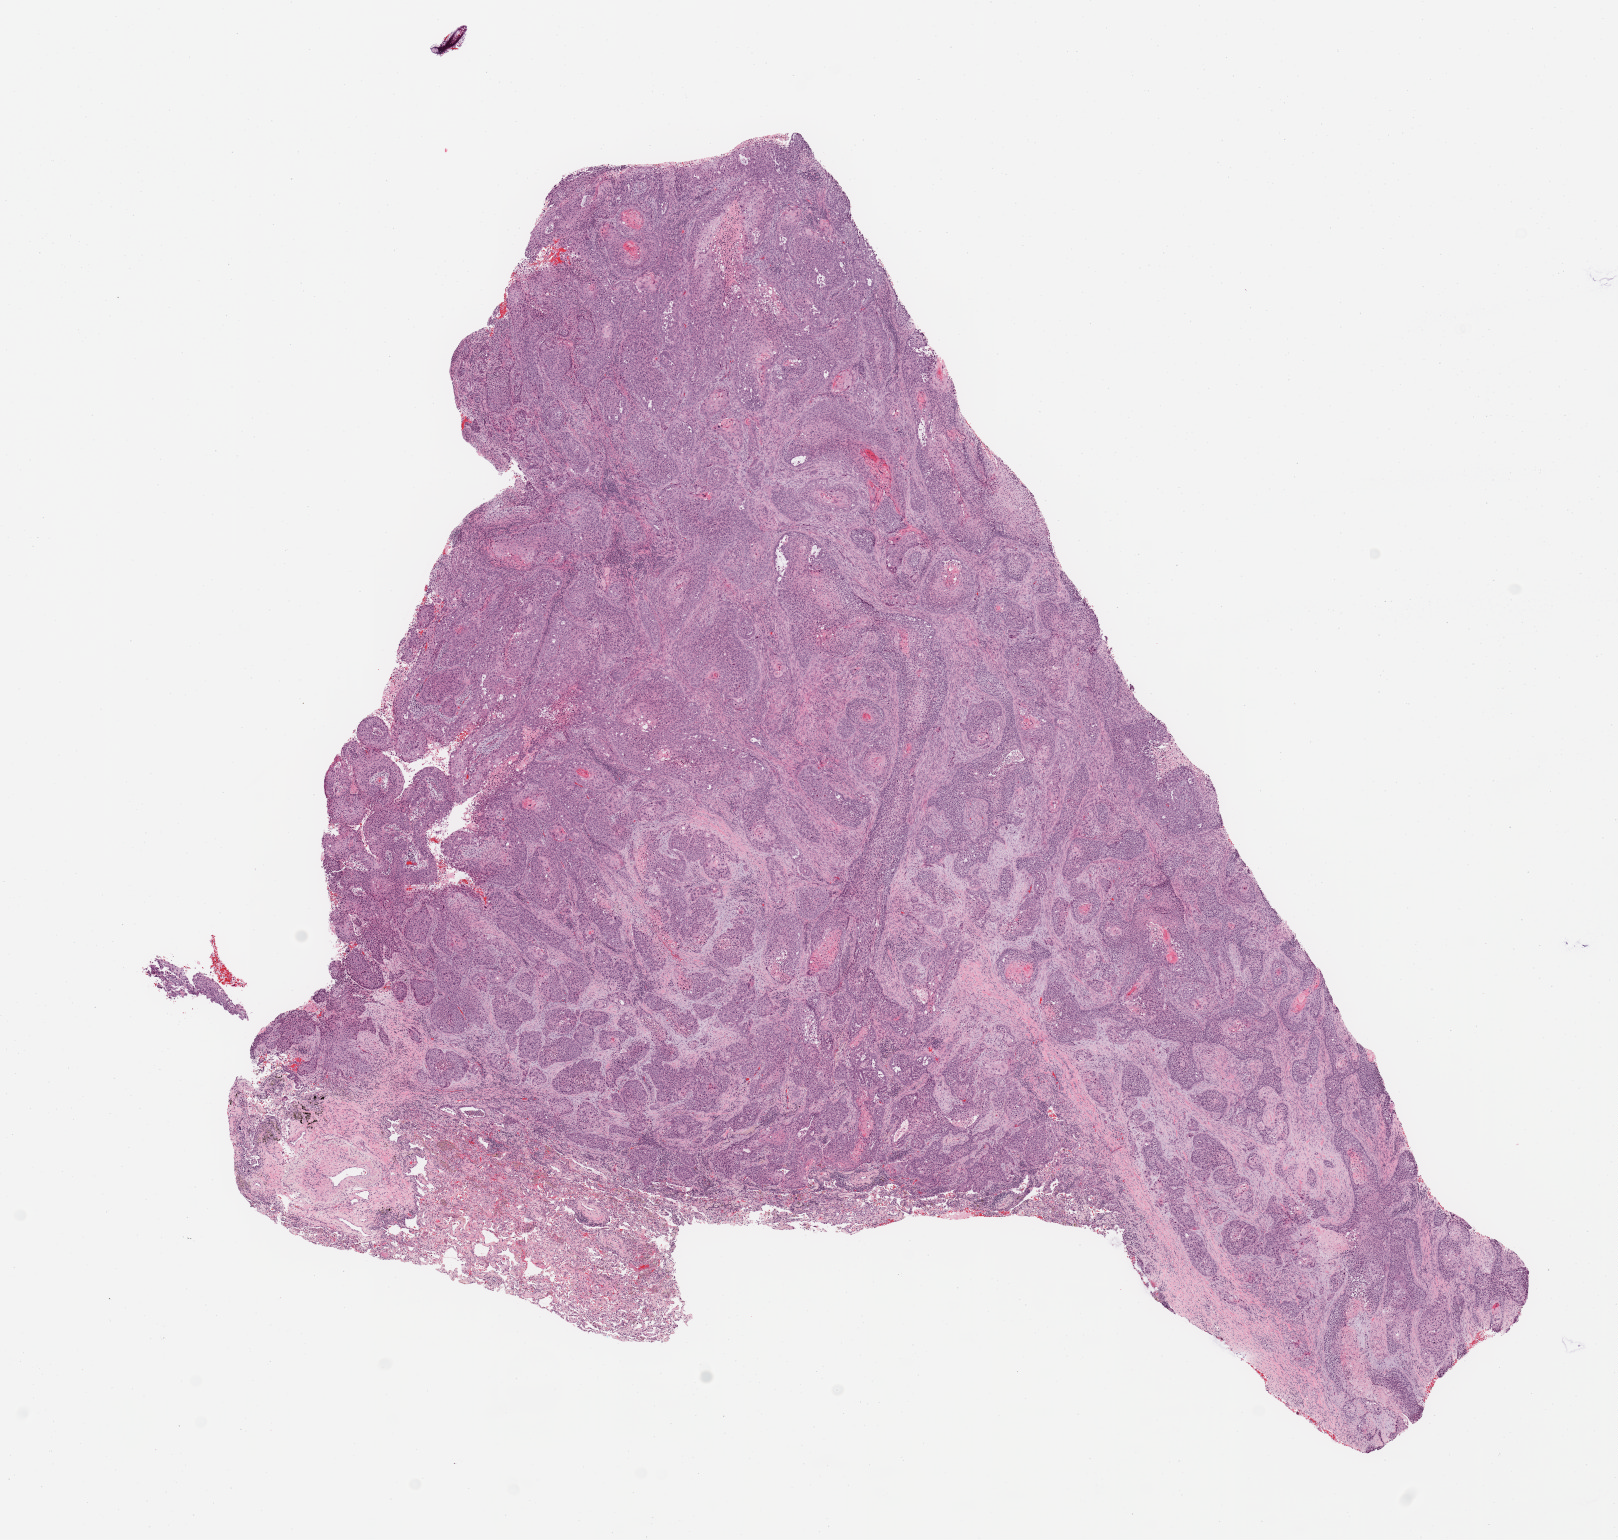
H&E-stained whole-slide image — shown as a low-resolution overview of the whole scanned area (about 12.8 x 12.2 mm, from a 20x scan); tumour tissue sample, sampled site: lung. Female, 61 y/o. Histologic grade: G2 (moderately differentiated). Pathologist review of this section (percent, as recorded): tumour nuclei 75%, necrosis 5%.
* AJCC pathologic stage: IIA
* histologic diagnosis: Squamous cell carcinoma, NOS
* primary tumour site (as recorded): left lower lobe